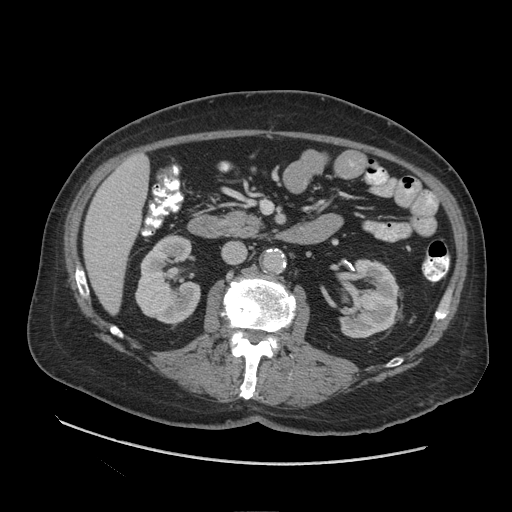
Contrast-enhanced abdominal CT (liver protocol), one axial slice. Reconstruction kernel STANDARD. 140 kVp. Soft-tissue window (W 400 / L 40 HU). 512 × 512 image matrix, field of view 420 × 420 mm. Case-level facts recorded for this patient, not image findings: diagnosis: hepatocellular carcinoma (patient treated with transarterial chemoembolisation; whether this scan precedes or follows treatment is not stated here); TNM stage (as recorded): Stage-I; Child-Pugh class: A.
Structures marked on this image (semi-automatically segmented with operator editing):
- liver parenchyma outside the tumour (the mass and vessels are separate outlines, so this box may not span the whole liver): bounding box (x1, y1, x2, y2) in pixels: (84, 154, 148, 312)